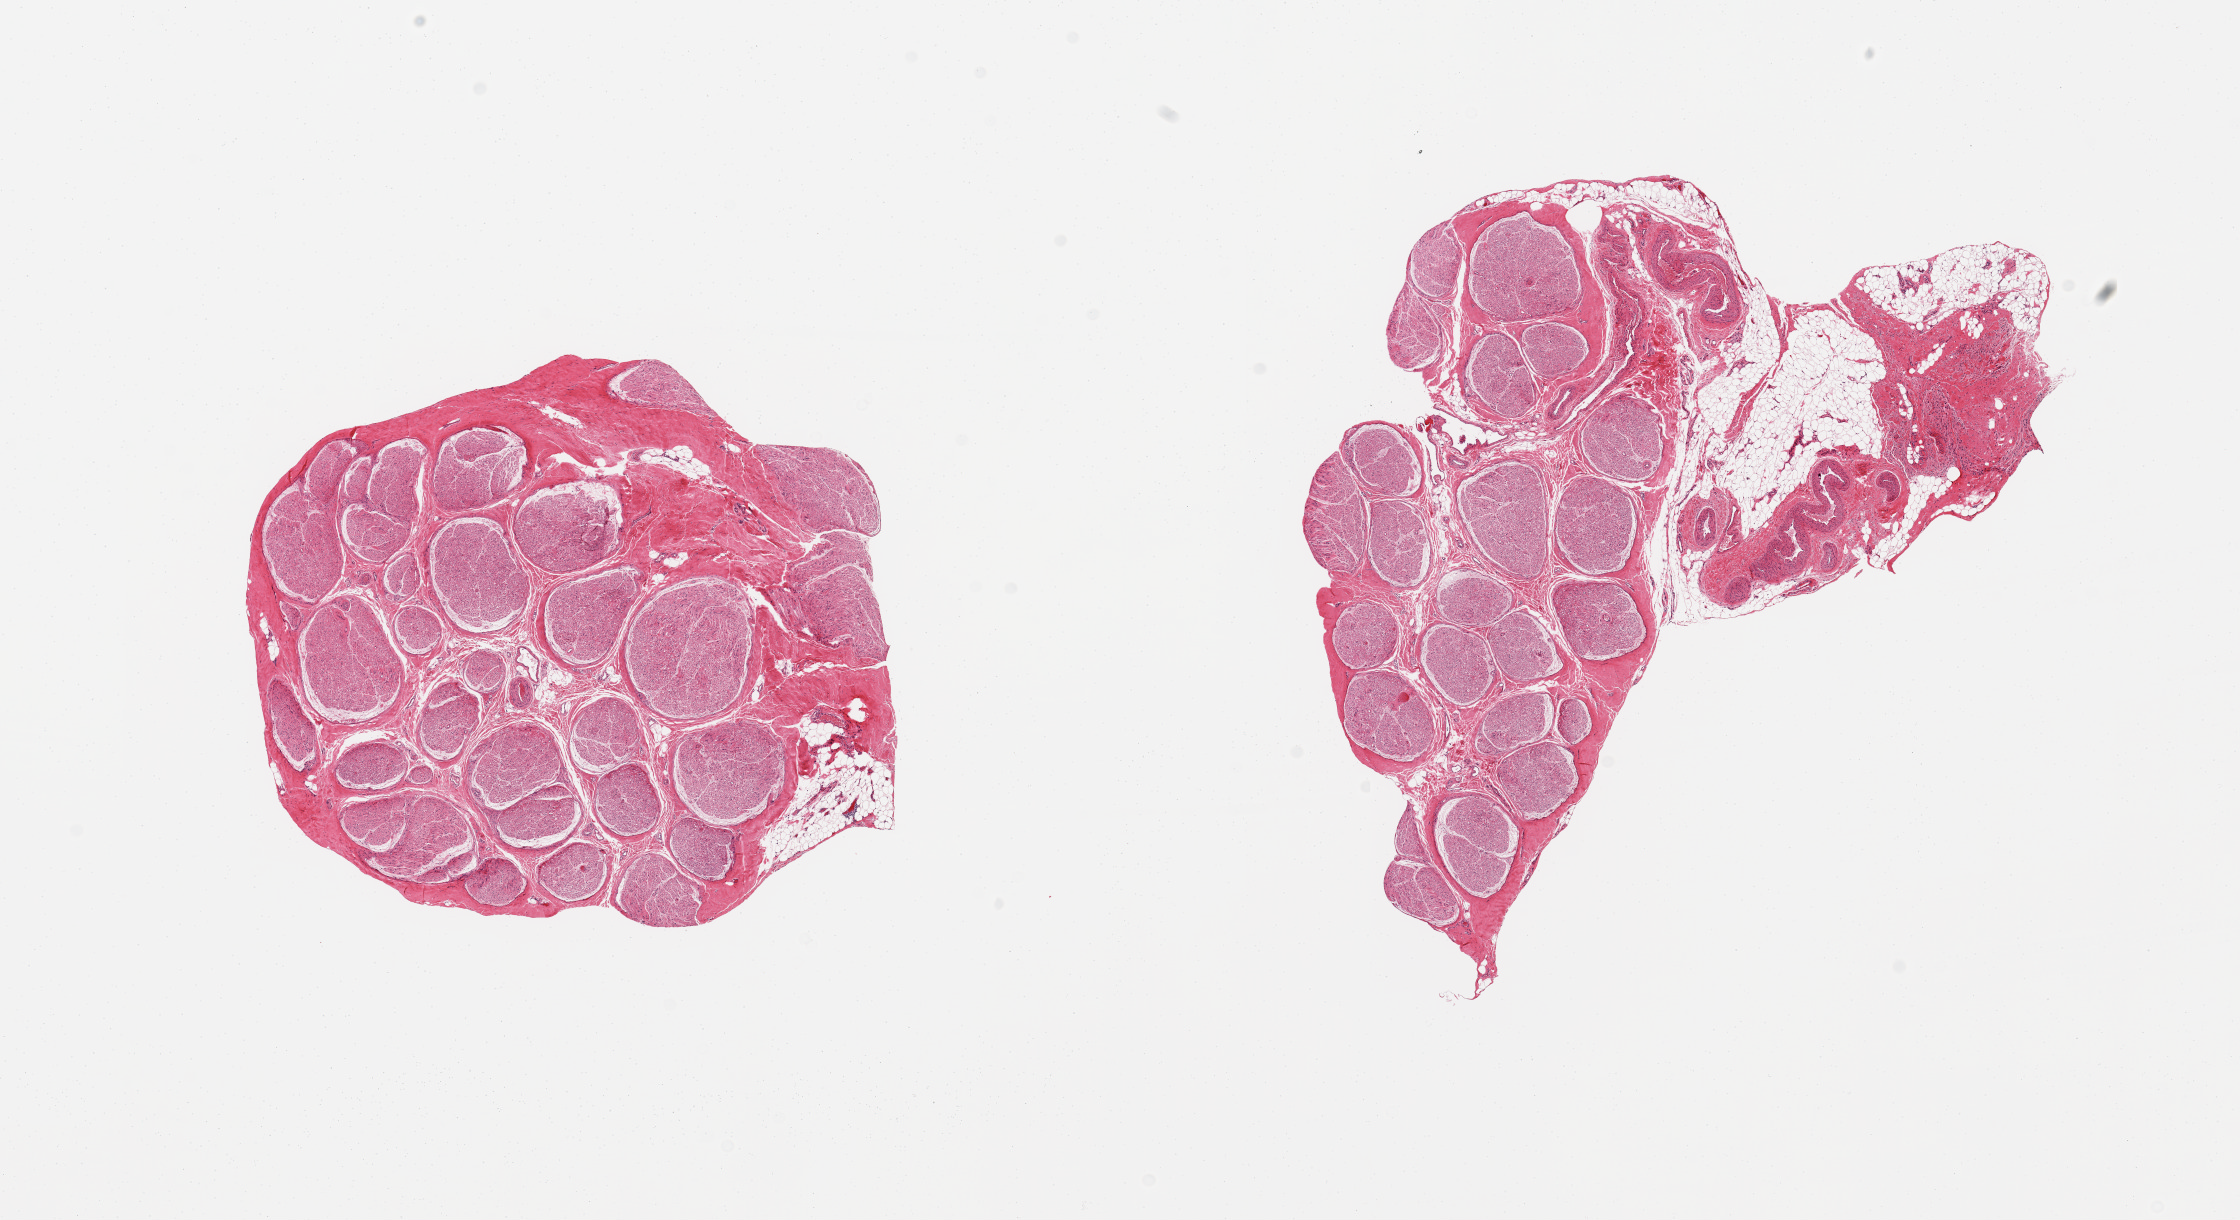
H&E whole-slide image, brightfield — shown as a low-resolution overview of the whole scanned area (about 17.7 x 9.7 mm), PAXgene-fixed paraffin-embedded (PFPE) section, section of tibial nerve (target tissue), donor tissue sample.
Review note (as recorded): 2 pieces; 1 piece has 40% external fibroadipose tissue.